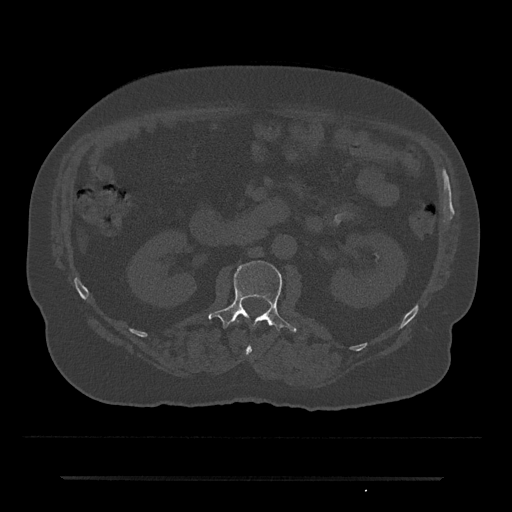
CT including the spine, one axial slice. Slice 21 of 797 in the series (ordered by position). Reconstruction kernel Br40s/3. 120 kVp. Bone window (W 1800 / L 400 HU). 0.5 mm slice thickness. 512 × 512 image matrix. Patient: male, 69 years. From the clinical record (not read from this slice): primary cancer: prostate.
Outlined on this slice (semi-automatic segmentation, software-assisted and operator-edited):
- L1 vertebra: bounding box [x1, y1, x2, y2] px = [236, 317, 252, 356]
- L2 vertebra: [208, 261, 297, 332]